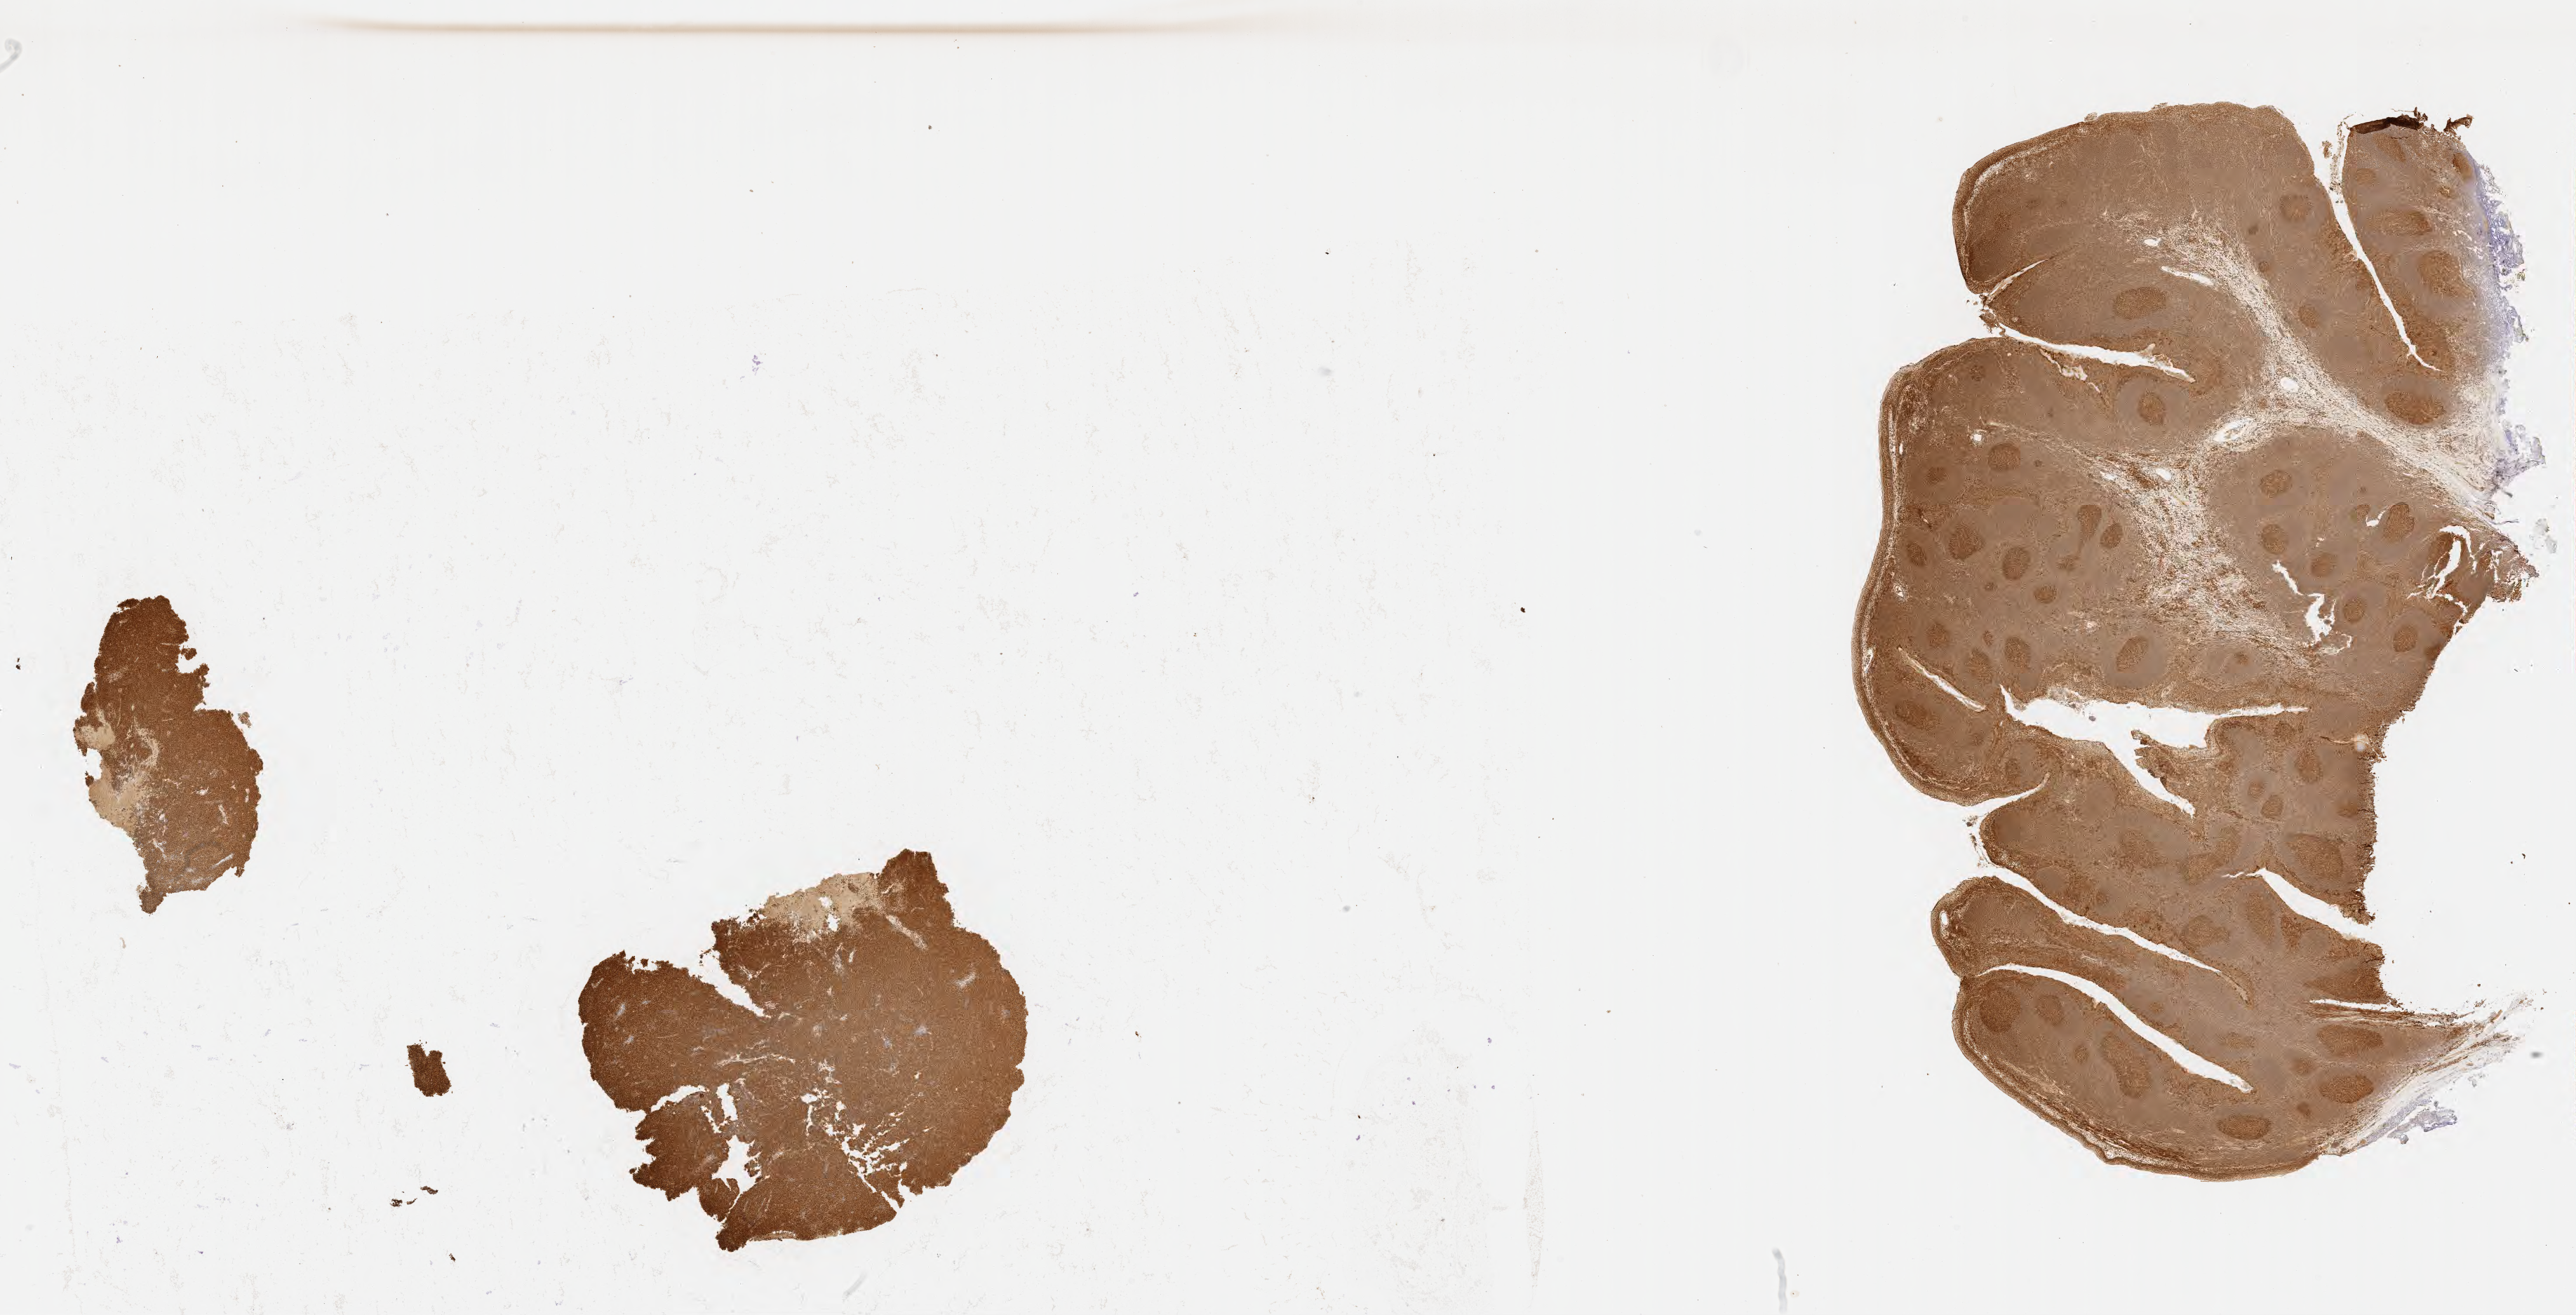
Immunohistochemistry (IHC) whole-slide image stained for BCL6 — whole scanned area (about 29.7 x 15.2 mm) shown as a low-resolution overview. Specimen: tumor tissue. Anatomic site: lymph node. Female patient, age 51 years.
Diagnosis: Diffuse large B-cell lymphoma, NOS.